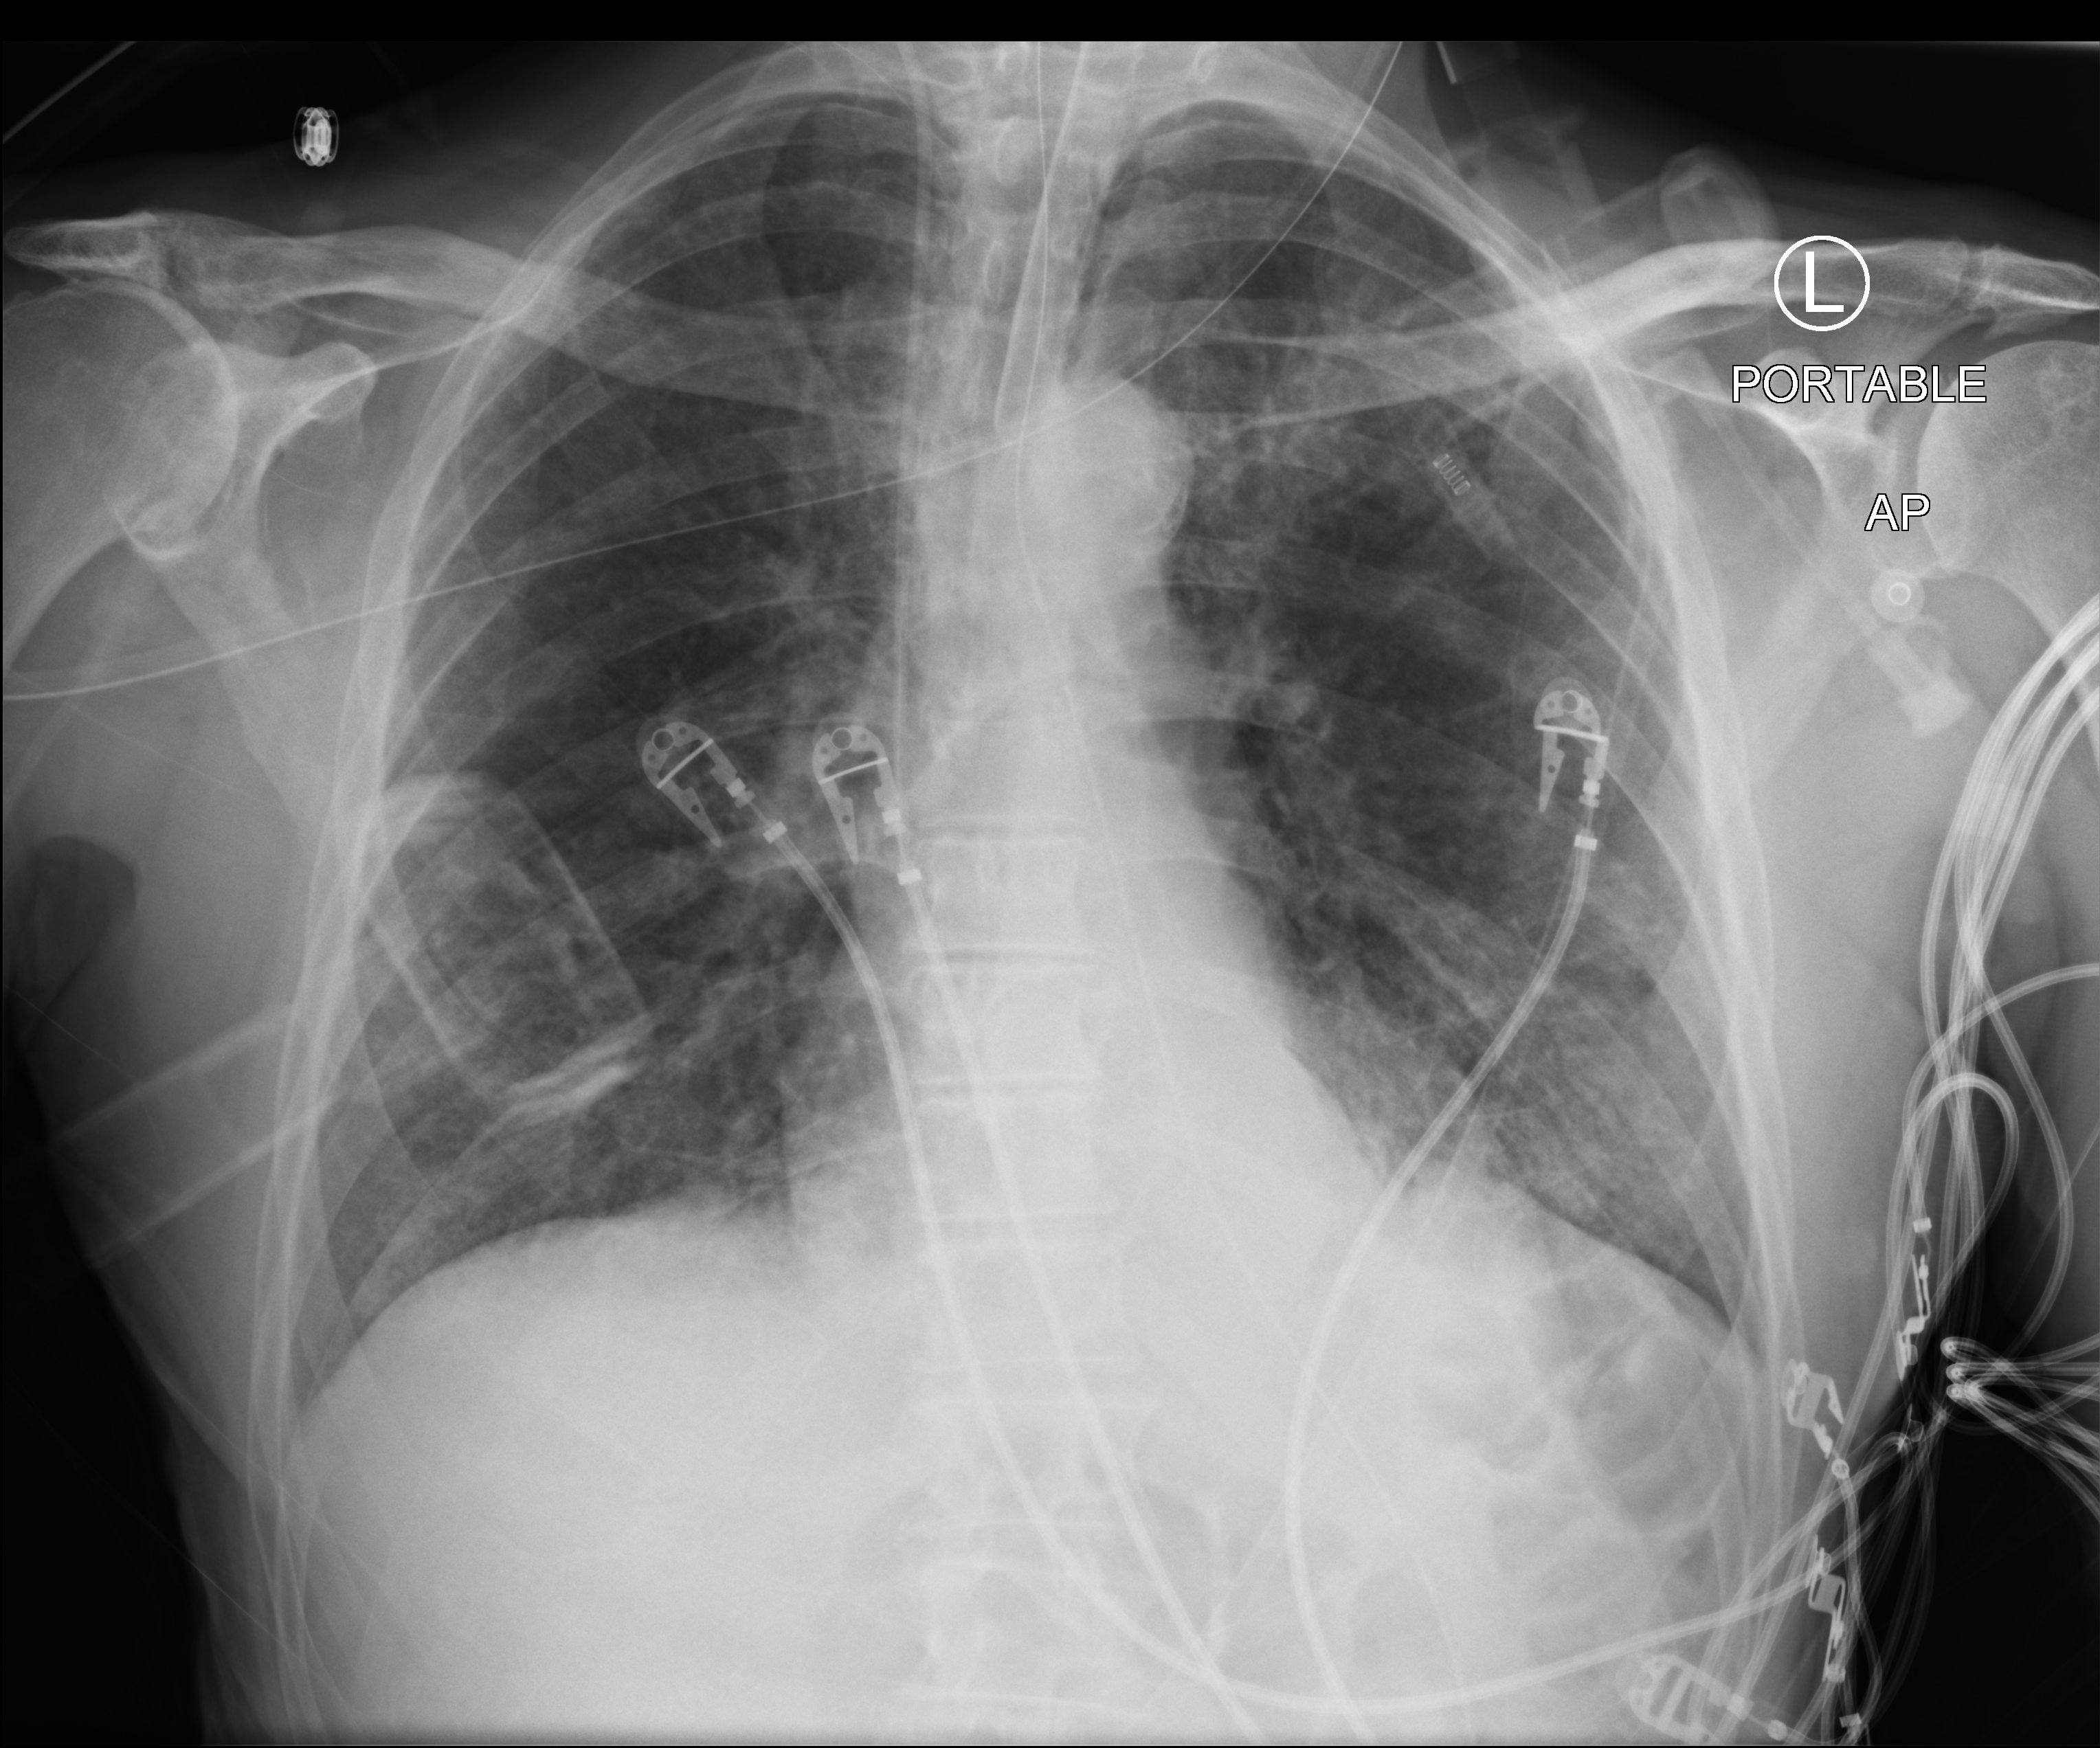
Chest X-ray (portable), anteroposterior (AP) projection. Patient hospitalised with COVID-19; male, aged 75–90 years.
Admission-level facts for this patient (not findings on this image; timing relative to this image not recorded):
- hypertension (admission record): yes
- admitted to intensive care during this hospital stay: yes